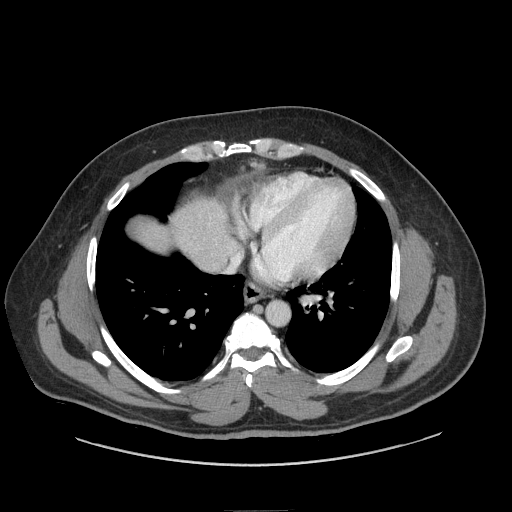
Contrast-enhanced abdominal CT (liver protocol), one axial slice; reconstruction kernel STANDARD; 140 kVp; soft-tissue window (W 400 / L 40 HU); 2.5 mm slice thickness; 512 × 512 image matrix. Case-level facts recorded for this patient, not image findings: diagnosis: hepatocellular carcinoma (patient treated with transarterial chemoembolisation; whether this scan precedes or follows treatment is not stated here); TNM stage (as recorded): Stage-II; Child-Pugh class: A; tumour differentiation: moderately differentiated; tumour nodularity: uninodular.
Outlined on this slice (semi-automatically segmented with operator editing):
- abdominal aorta: box from (x=266, y=302) to (x=289, y=326) px
- liver parenchyma outside the tumour (the mass and vessels are separate outlines, so this box may not span the whole liver): (x=134, y=200)–(x=230, y=262)